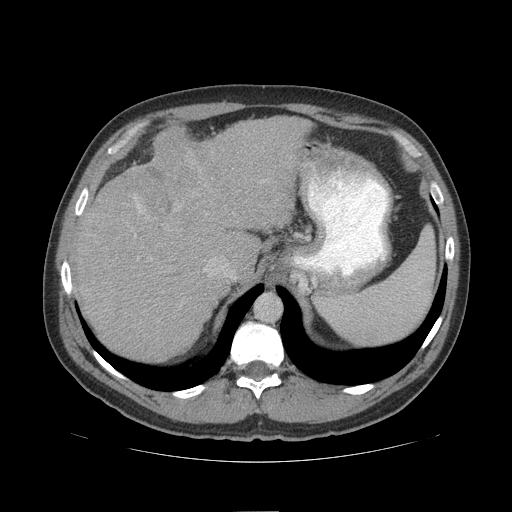
Contrast-enhanced abdominal CT (liver protocol), one axial slice. Slice 76 of 109 in the series (ordered by position). Soft-tissue window (W 400 / L 40 HU). 2.5 mm slice thickness. 512 × 512 image matrix, field of view 420 × 420 mm. From the clinical record (not read from this slice): diagnosis: hepatocellular carcinoma (patient treated with transarterial chemoembolisation; whether this scan precedes or follows treatment is not stated here); TNM stage (as recorded): Stage-IIIB; Child-Pugh class: A; tumour differentiation: poorly differentiated; tumour nodularity: multinodular.
Outlined on this slice (semi-automatic segmentation, software-assisted and operator-edited):
- abdominal aorta: bounding box [x1, y1, x2, y2] px = [255, 294, 281, 321]
- liver parenchyma outside the tumour (the mass and vessels are separate outlines, so this box may not span the whole liver): [72, 116, 310, 360]
- mass: [109, 124, 212, 233]